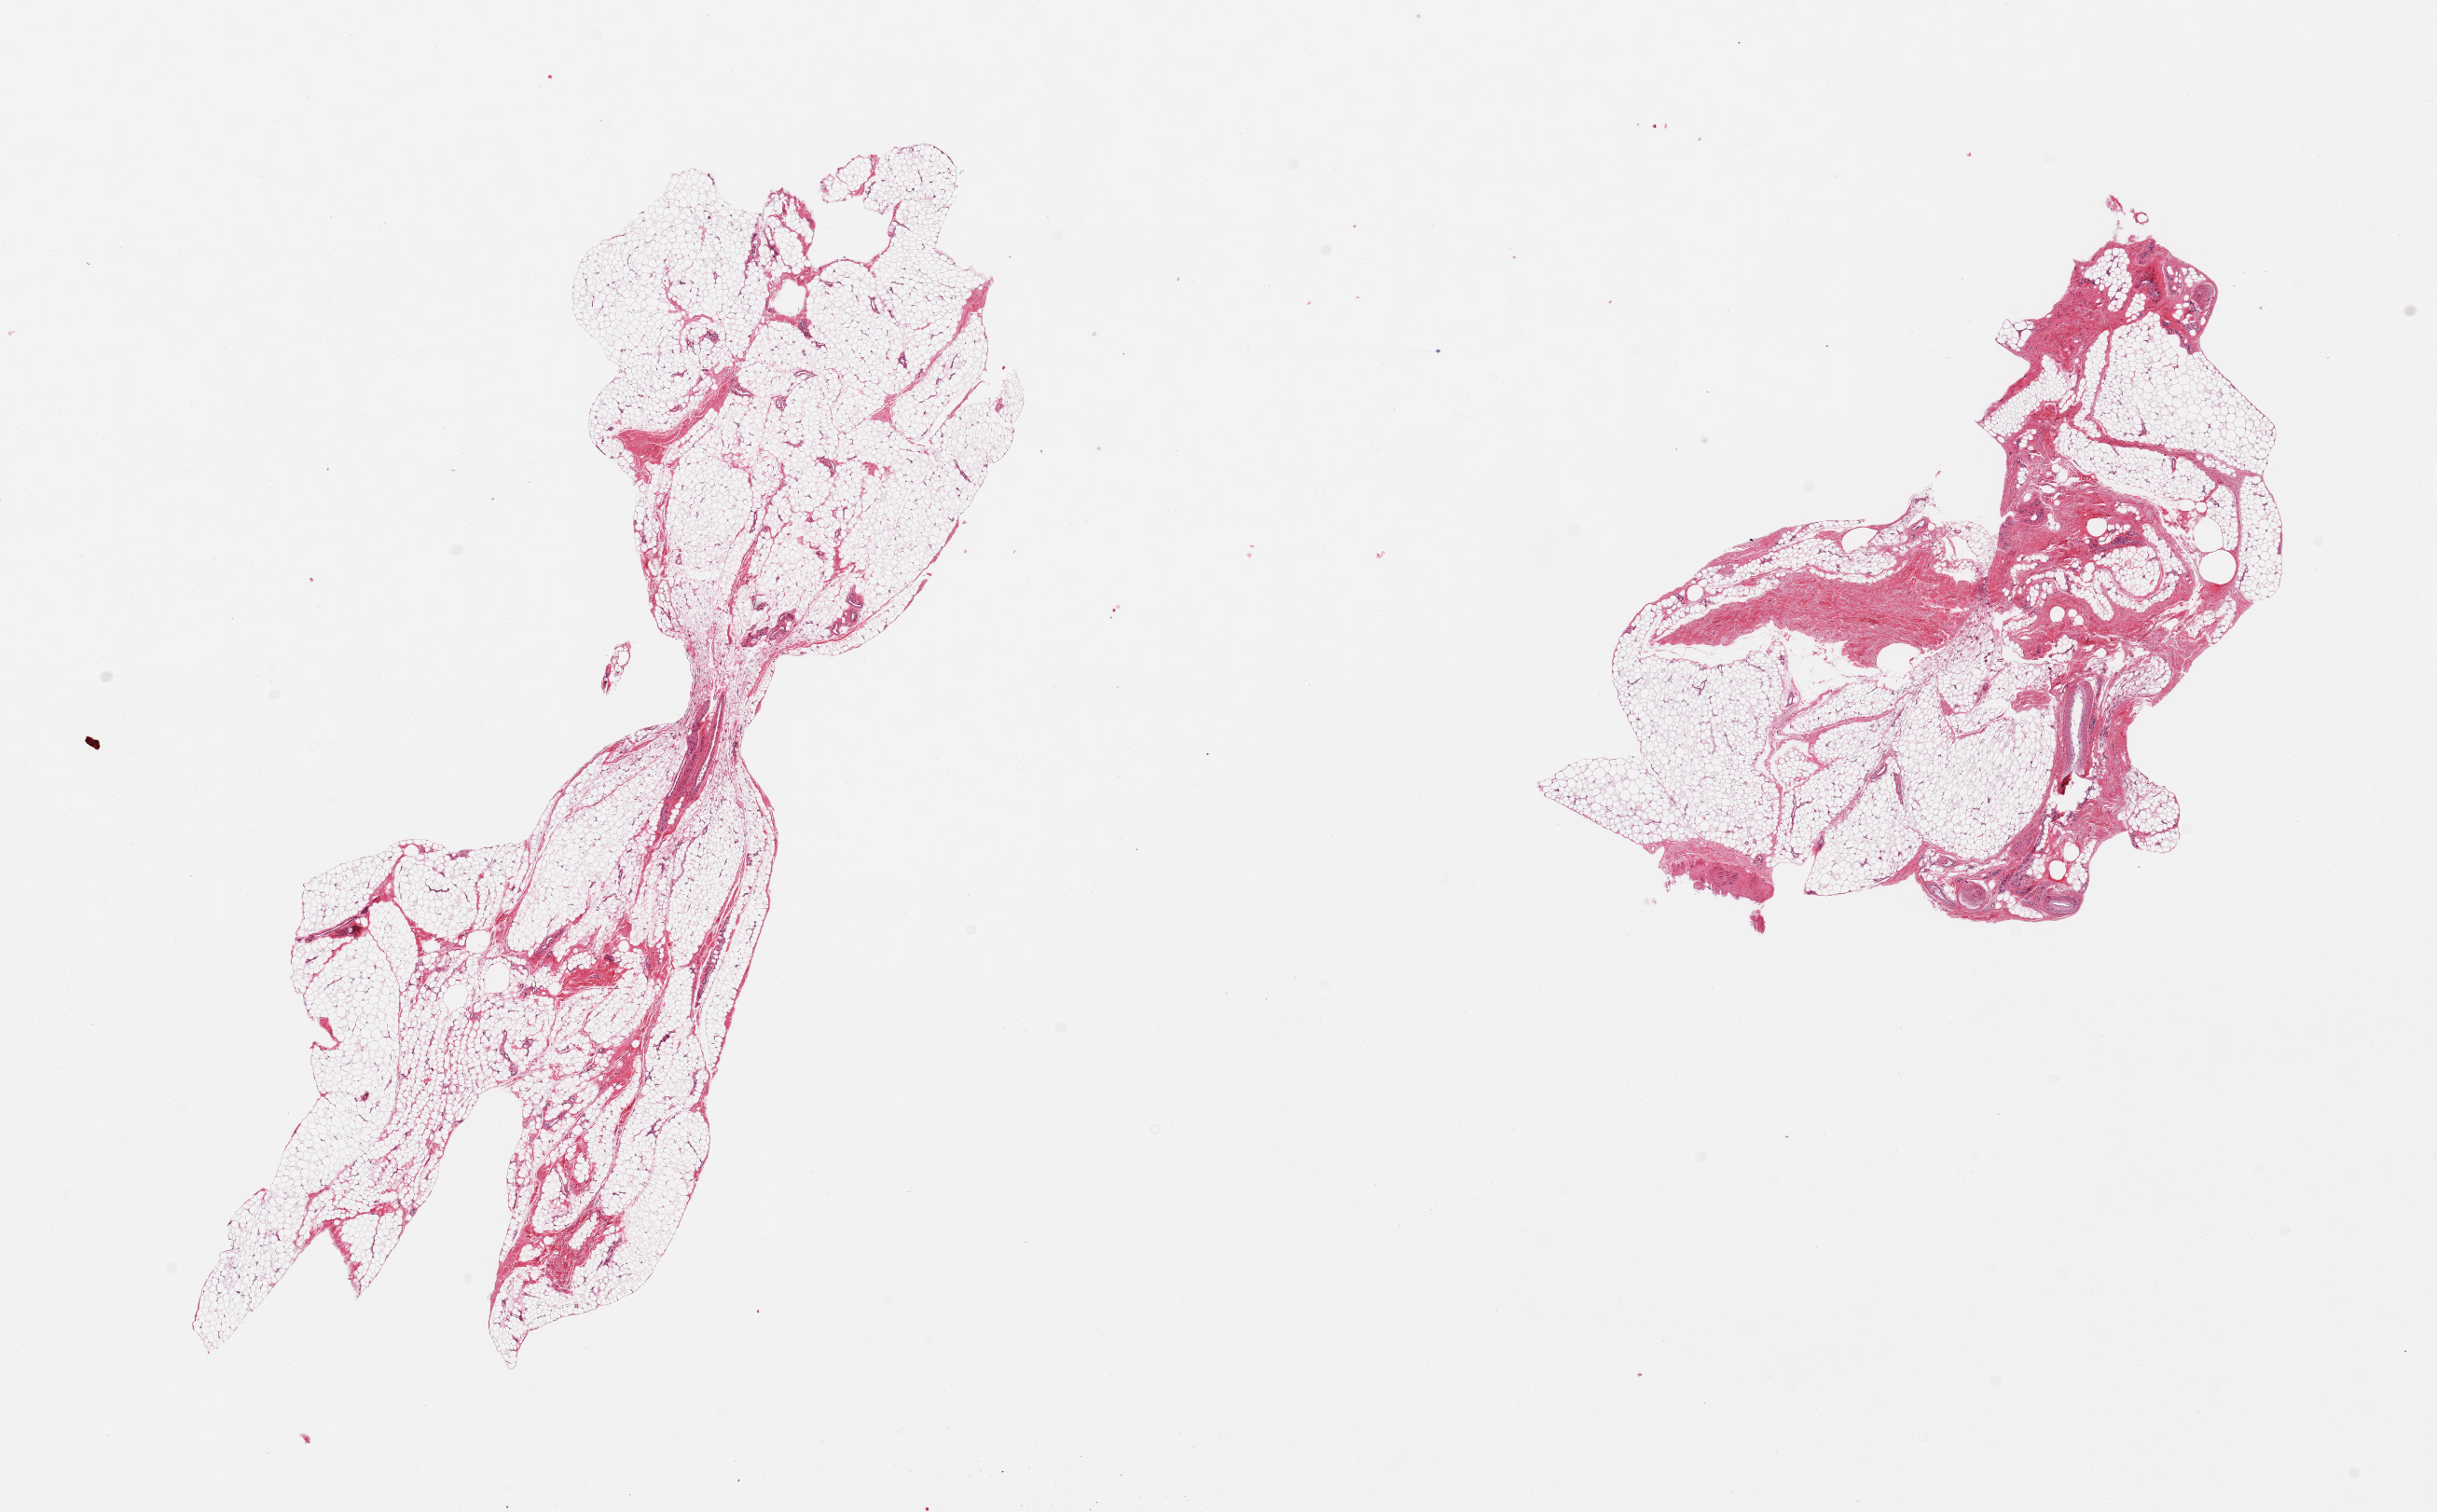
Whole-slide image, haematoxylin and eosin stain — shown as a low-resolution overview of the whole scanned area (about 20.7 x 12.8 mm), PAXgene-fixed paraffin-embedded (PFPE) section, target tissue: adipose tissue, donor tissue sample. Donor sex: male.
• pathologist's review note for this sample: 2 pieces; 10 & 20% fibrous content